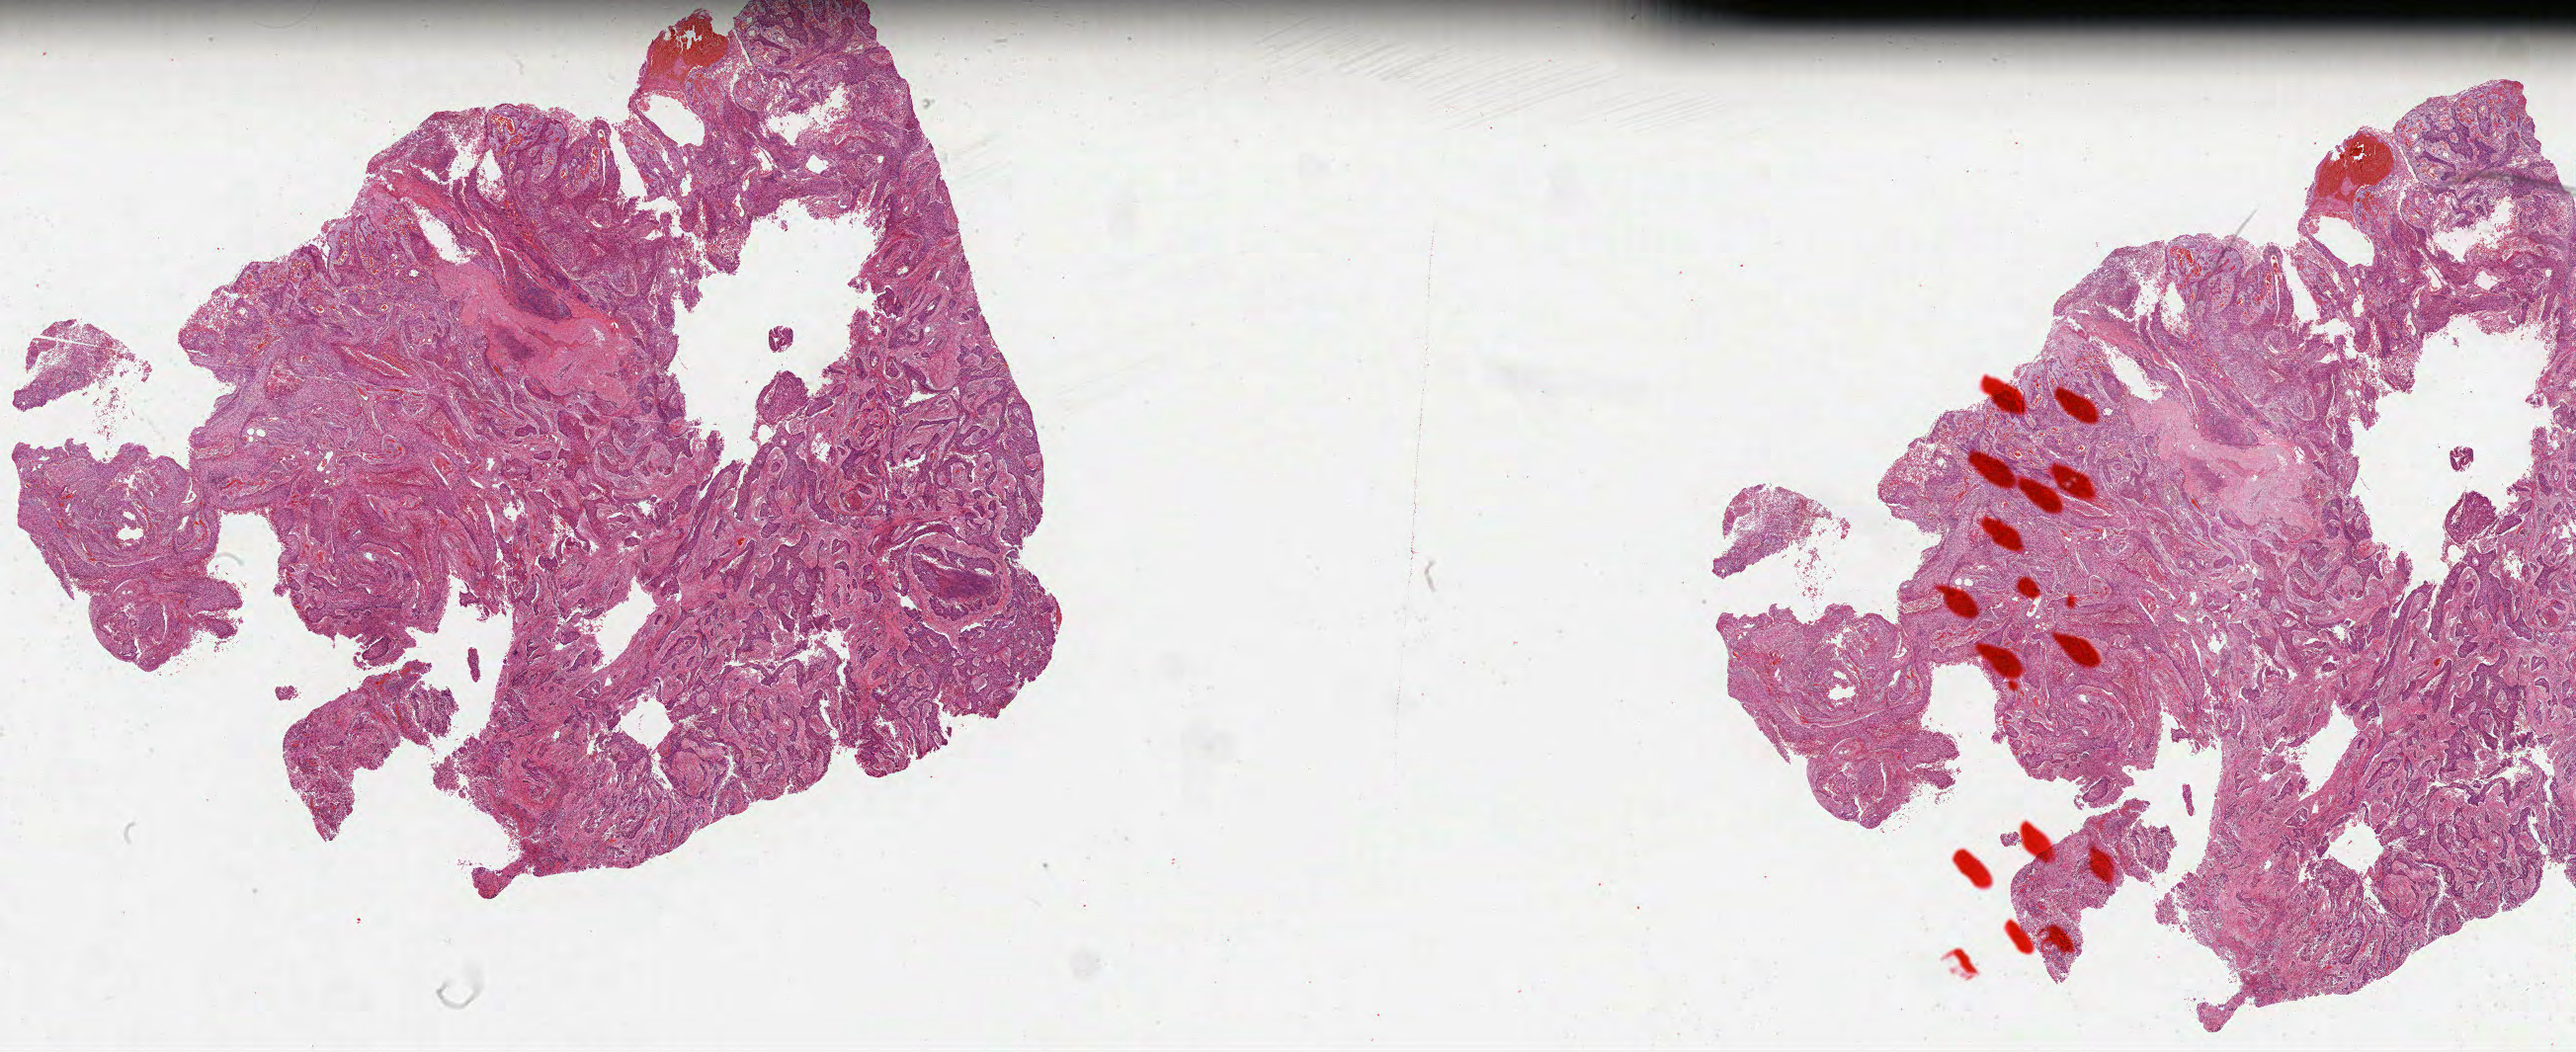
Digitized Hematoxylin and eosin (H&E) stained tissue section (whole slide), whole scanned area (about 42.1 x 17.2 mm, slide scanned at 40x) shown as a low-resolution overview, formalin-fixed paraffin-embedded (FFPE) diagnostic section, primary tumour sample from the lung. Female, age 60 years at initial diagnosis.
Laterality: right. AJCC pathologic stage: IIB (6th edition). Histologic diagnosis: Squamous cell carcinoma, NOS.